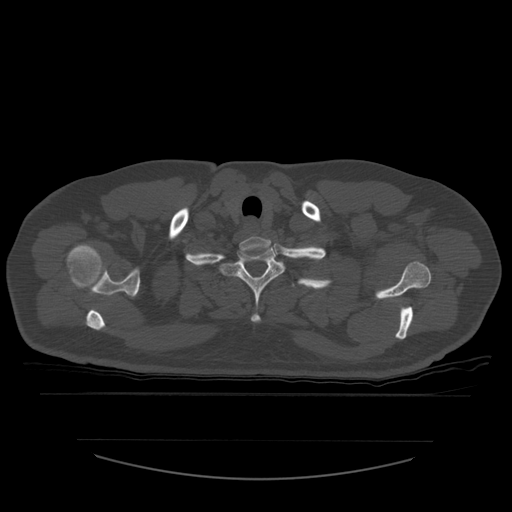
CT including the spine, one axial slice. Slice 469 of 532 in the series (ordered by position). Bone window (W 1800 / L 400 HU). 512 × 512 image matrix, field of view 441 × 441 mm. Patient age 44 years. From the clinical record (not read from this slice): primary cancer: soft tissue sarcoma.
Outlined on this slice (semi-automatic segmentation, software-assisted and operator-edited):
- T1 vertebra: bounding box [x1, y1, x2, y2] px = [220, 245, 285, 323]
- T2 vertebra: [292, 280, 313, 288]